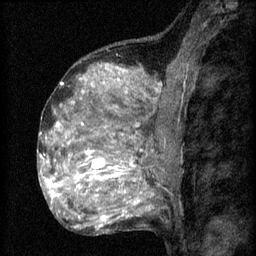
Breast MRI (dynamic contrast-enhanced), one sagittal slice. Slice 39 of 60 in the series (ordered by position). 3 images stored at this slice position (order not interpretable as contrast timing). 1.5 T. TE 4.2 ms, TR 8.2 ms. 2 mm slice thickness. 256 × 256 image matrix. Patient: female, 48 years.
Outlined on this slice (semi-automatic segmentation, software-assisted and operator-edited):
- analysis volume of interest (the breast-tissue region the enhancement analysis was run in; not a lesion): box from (x=61, y=138) to (x=153, y=201) px
- tumour enhancement mask (voxels above the 70 % enhancement threshold inside the analysis volume of interest): (x=75, y=150)–(x=140, y=201)